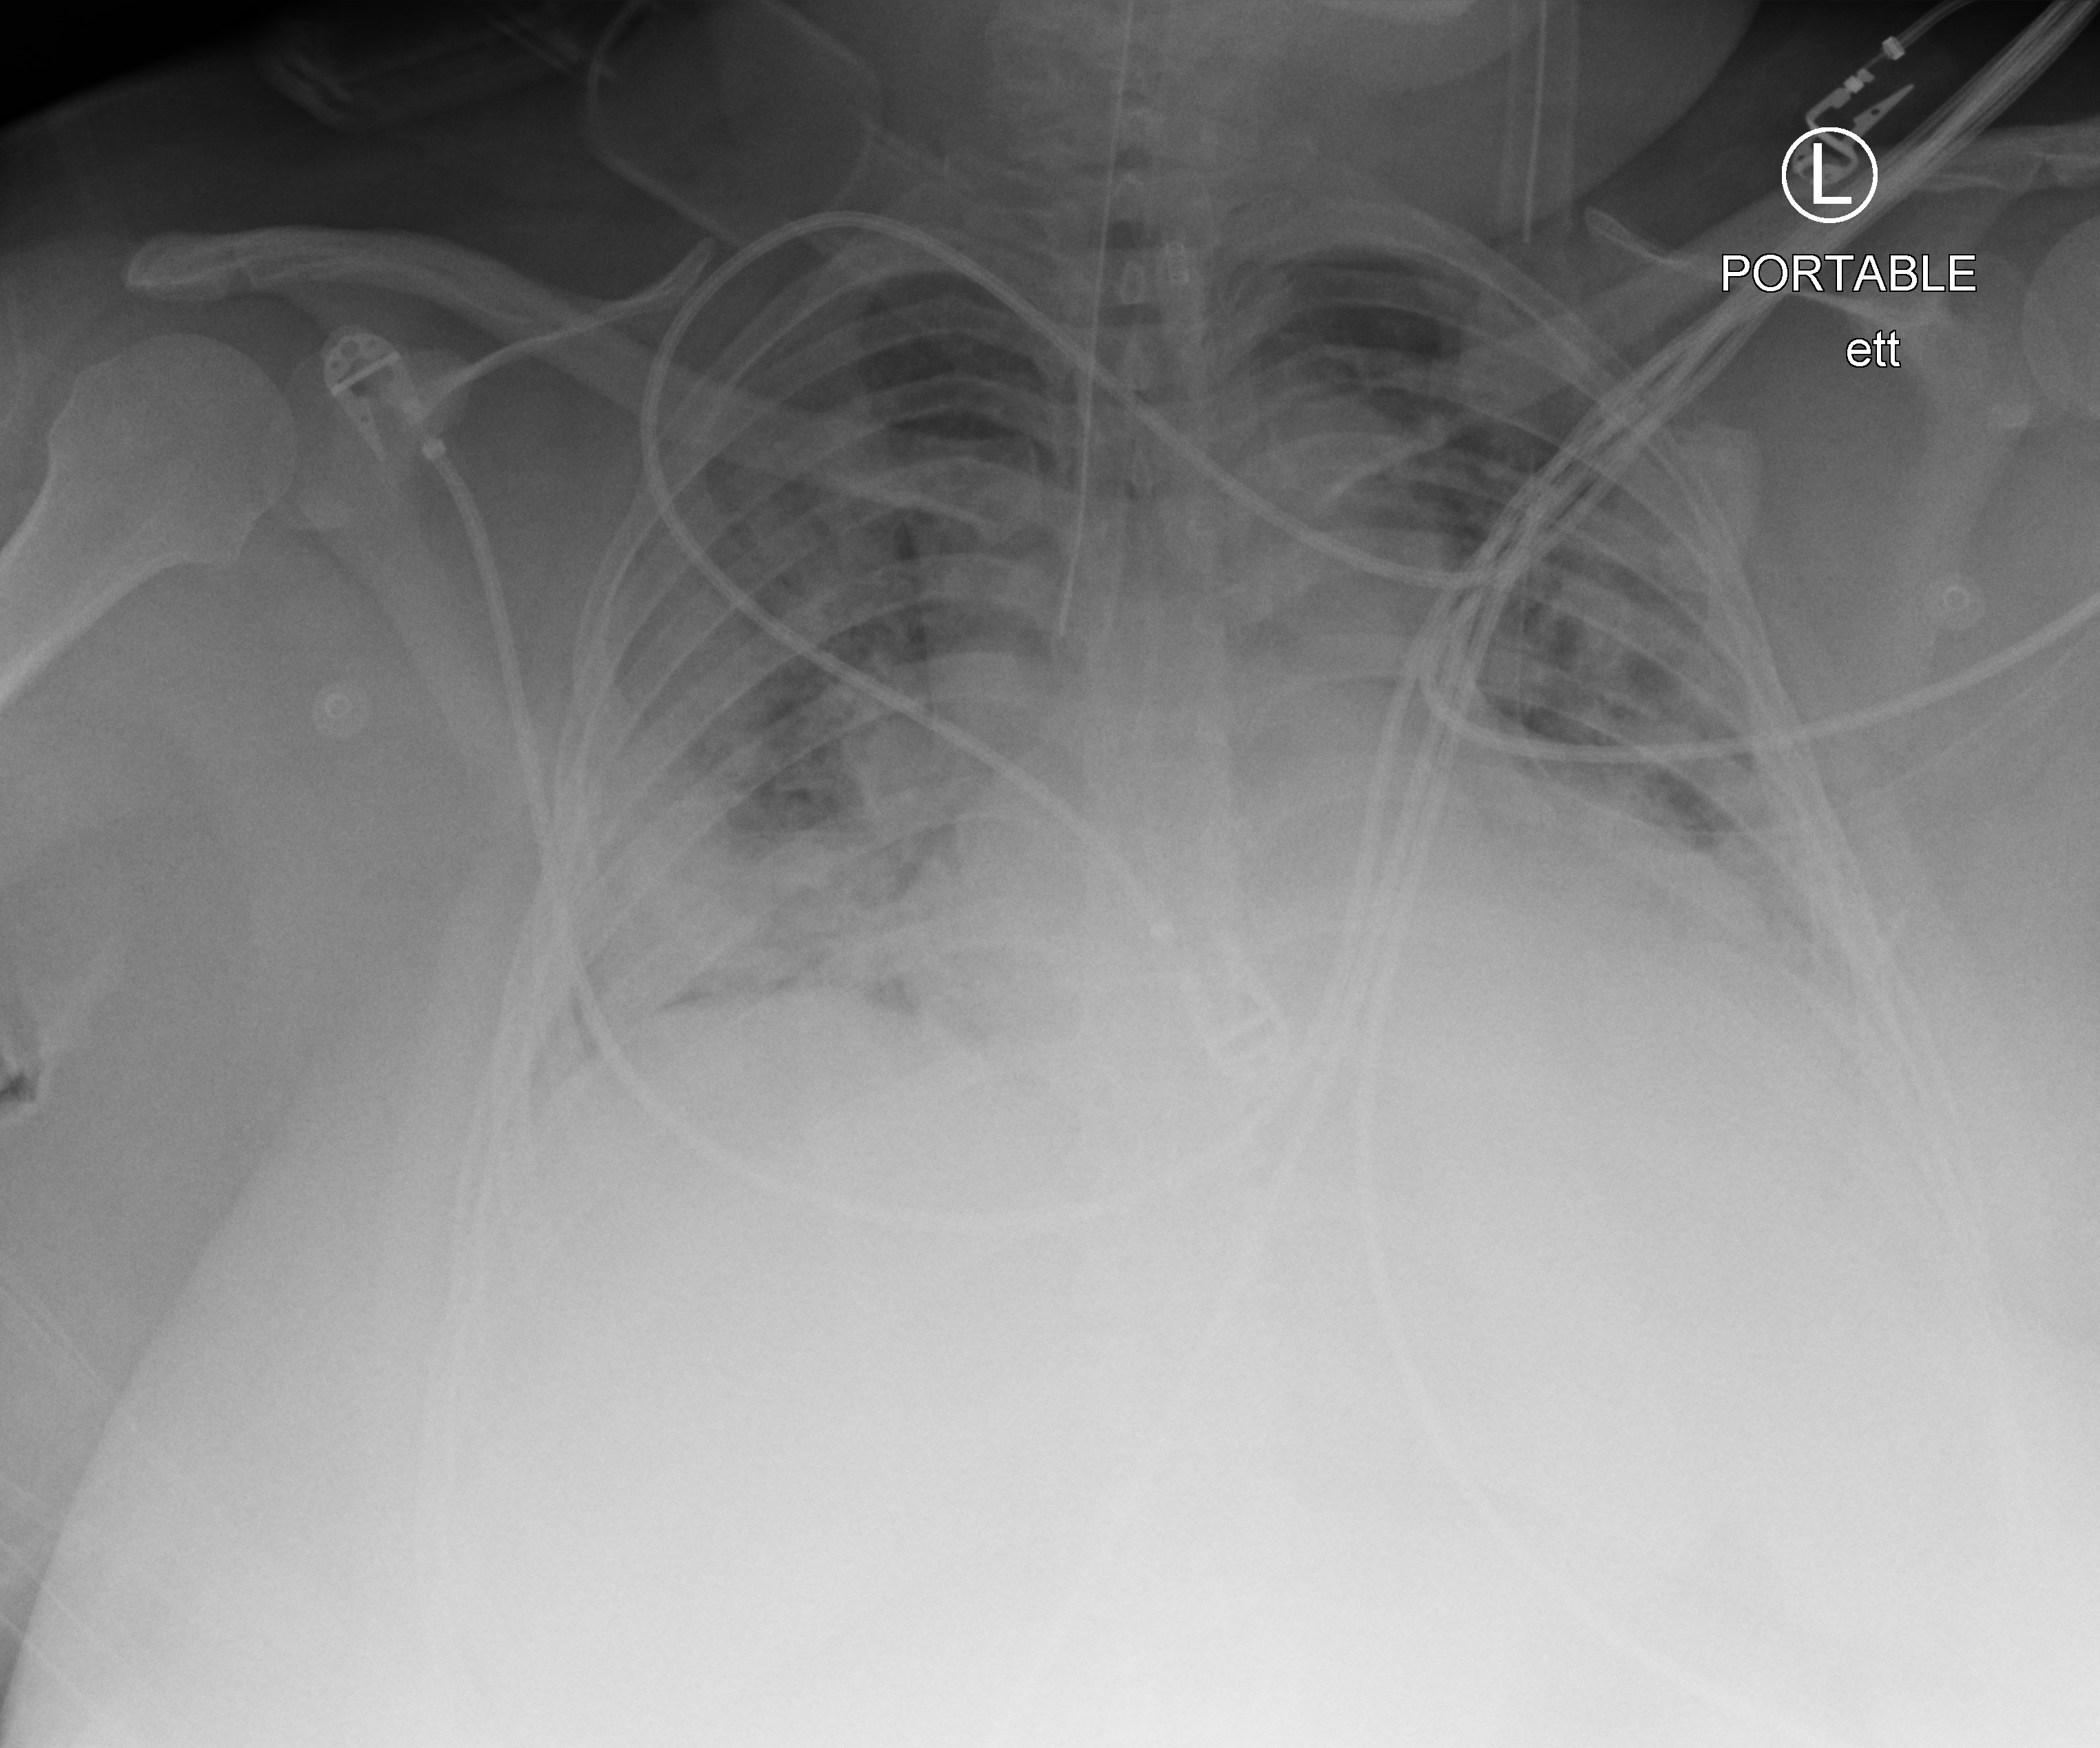
Bedside chest radiograph (computed radiography); anteroposterior (AP) projection. Female patient hospitalised with COVID-19, age 18–59 years.
Admission-level facts for this patient (not findings on this image; timing relative to this image not recorded):
- admitted to intensive care during this hospital stay: yes
- length of hospital stay: 23 days